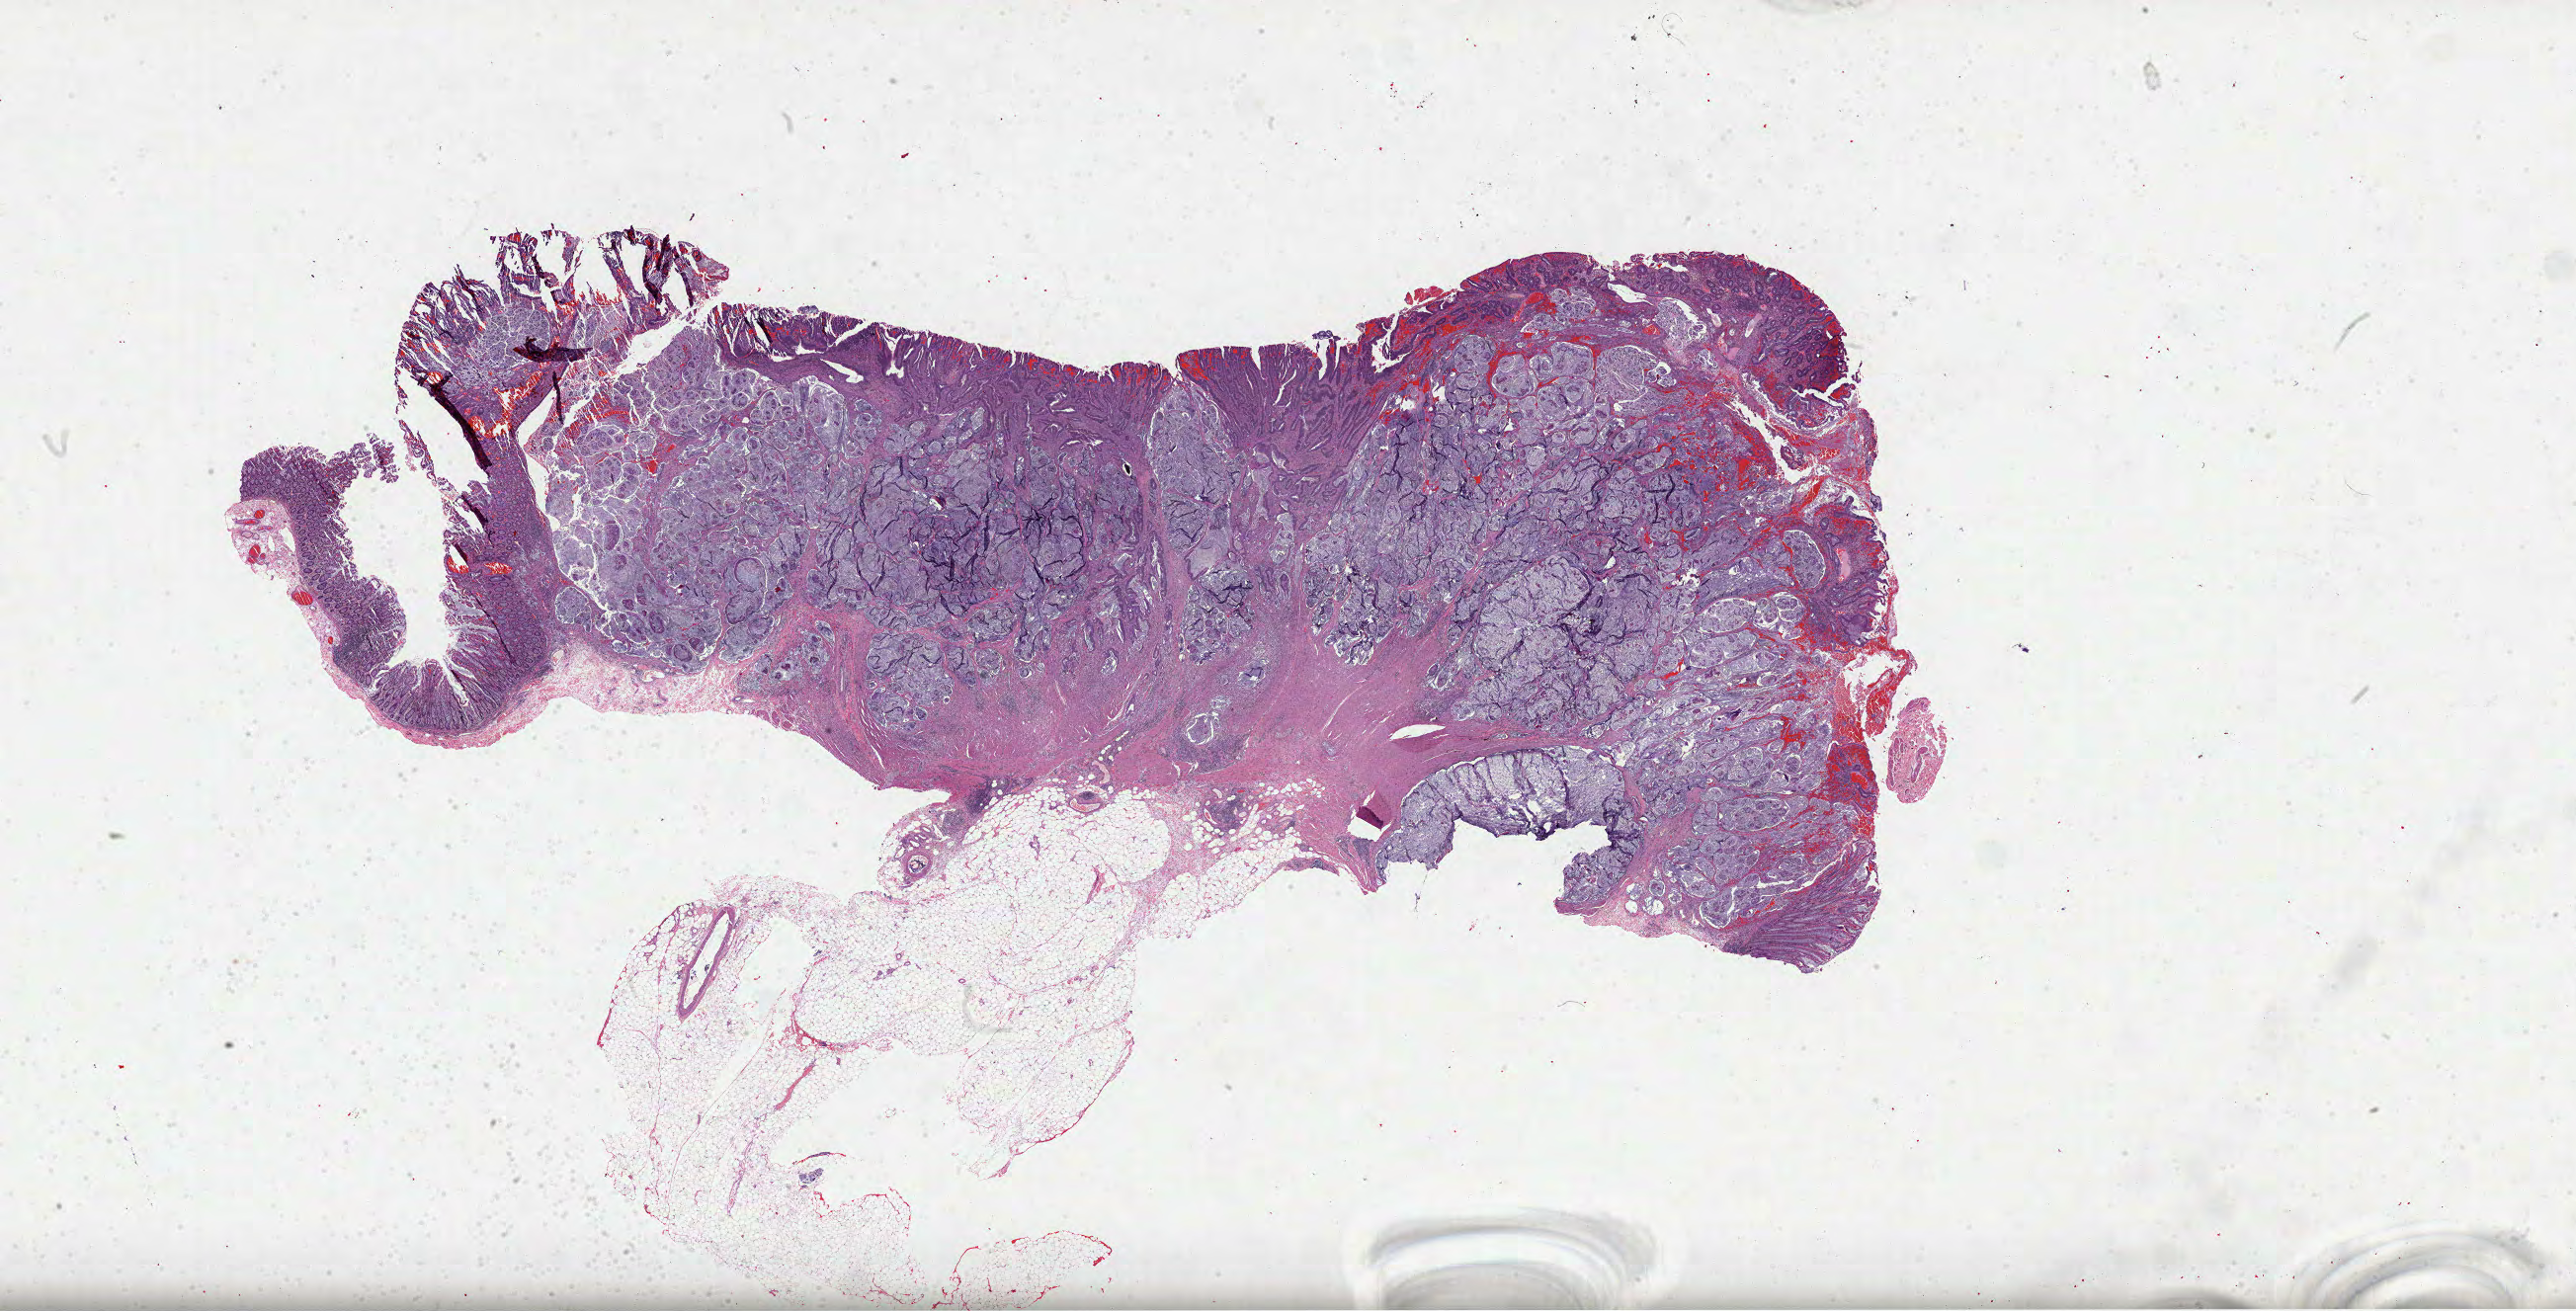
Hematoxylin and eosin (H&E) stained whole-slide image — whole scanned area (about 42.1 x 21.4 mm, from a 40x scan) shown as a low-resolution overview; formalin-fixed paraffin-embedded (FFPE) diagnostic section; primary tumour sample from the colon. Female patient; age at initial diagnosis 48 years.
AJCC pathologic stage: IIIB (7th edition). Lymph nodes positive (case pathology): 1 of 46 examined. Diagnosis: Mucinous adenocarcinoma.